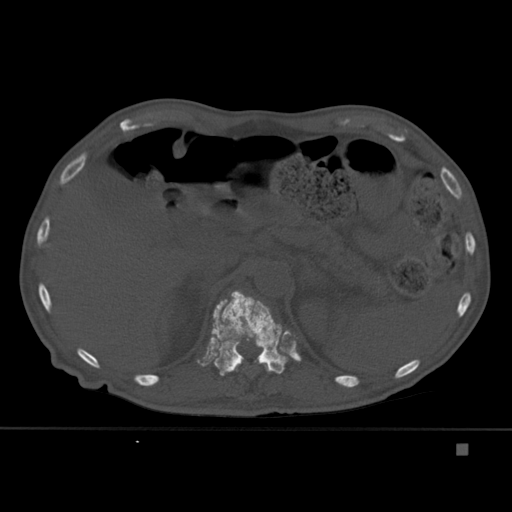
CT including the spine, one axial slice. Slice 203 of 451 in the series (ordered by position). Bone window (W 1800 / L 400 HU). 1.5 mm slice thickness. 512 × 512 image matrix. Male patient, age 75 years. From the clinical record (not read from this slice): primary cancer: prostate.
Annotated regions visible in this slice (semi-automatically segmented with operator editing):
- T11 vertebra: bounding box (x1, y1, x2, y2) in pixels: (232, 360, 271, 372)
- T12 vertebra: (210, 290, 288, 376)